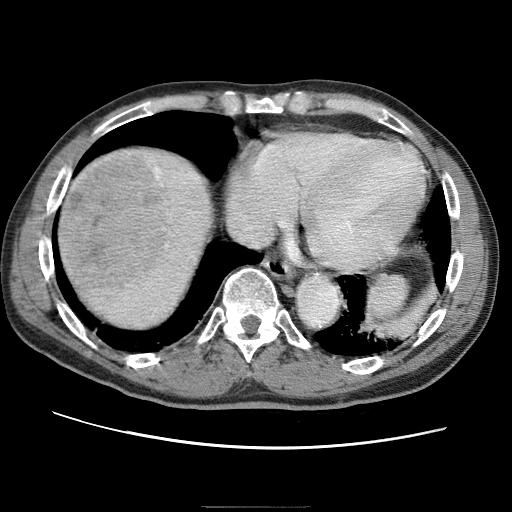
Contrast-enhanced abdominal CT (liver protocol), one axial slice. Slice 62 of 75 in the series (ordered by position). One of 2 acquisitions stored at this slice position. Soft-tissue window (W 400 / L 40 HU). 2.5 mm slice thickness. 512 × 512 image matrix. From the clinical record (not read from this slice): diagnosis: hepatocellular carcinoma (patient treated with transarterial chemoembolisation; whether this scan precedes or follows treatment is not stated here); TNM stage (as recorded): Stage-II; Child-Pugh class: A; tumour differentiation: well differentiated.
Annotated regions visible in this slice (semi-automatic segmentation, software-assisted and operator-edited):
- liver parenchyma outside the tumour (the mass and vessels are separate outlines, so this box may not span the whole liver): bounding box <56,146,216,332> (left, top, right, bottom; pixels)
- mass: <60,149,177,295>
- liver vessels: <75,167,195,269>